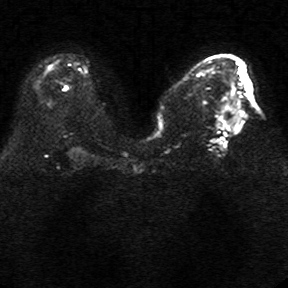
Breast MRI, one axial slice; slice 14 of 34 in the series (ordered by position); diffusion-weighted series; image 2 of 4 stored at this slice position (different b-values; order by instance number); 1.5 T; 5 mm slice thickness; 288 × 288 image matrix. Female patient.
Annotated regions visible in this slice (outlined manually by an expert reader):
- tumour on diffusion-weighted imaging: bounding box [x1, y1, x2, y2] px = [224, 105, 242, 122]